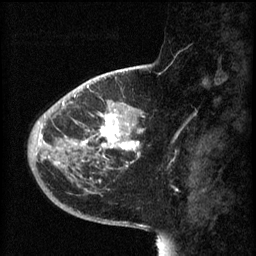
Breast MRI (dynamic contrast-enhanced), one sagittal slice; slice 20 of 60 in the series (ordered by position); 3 images stored at this slice position (order not interpretable as contrast timing); 1.5 T; TE 4.2 ms, TR 8.1 ms; 2 mm slice thickness; 256 × 256 image matrix, field of view 200 × 200 mm. Patient: female, 44 years.
Outlined on this slice (semi-automatic segmentation, software-assisted and operator-edited):
- analysis volume of interest (the breast-tissue region the enhancement analysis was run in; not a lesion): bounding box (x1, y1, x2, y2) in pixels: (59, 110, 144, 169)
- tumour enhancement mask (voxels above the 70 % enhancement threshold inside the analysis volume of interest): (74, 112, 143, 161)